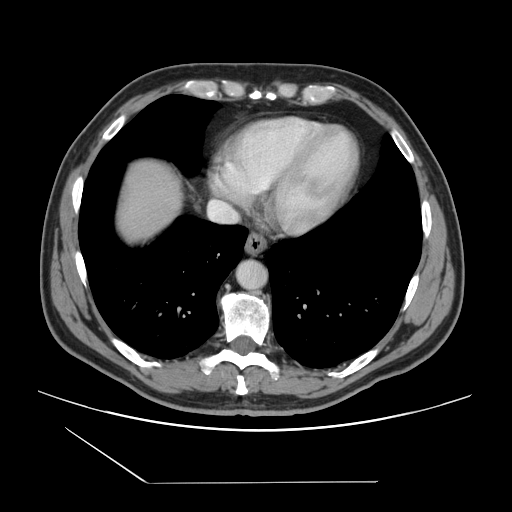
Contrast-enhanced abdominal CT, one axial slice. Slice 137 of 157 in the series (ordered by position). Intravenous contrast given. Soft-tissue window (W 400 / L 40 HU). 2.5 mm slice thickness. 512 × 512 image matrix, field of view 407 × 407 mm. Male patient, age 61 years. Case-level facts recorded for this patient, not image findings: diagnosis: colorectal cancer liver metastases, imaged before liver resection; multiple liver metastases: yes; largest metastasis: 5.5 cm; disease in both lobes: yes.
Structures marked on this image (outlined manually by an expert reader):
- liver: bounding box [x1, y1, x2, y2] px = [118, 163, 181, 240]
- planned liver remnant (the part of the liver to remain after resection): [118, 163, 180, 228]